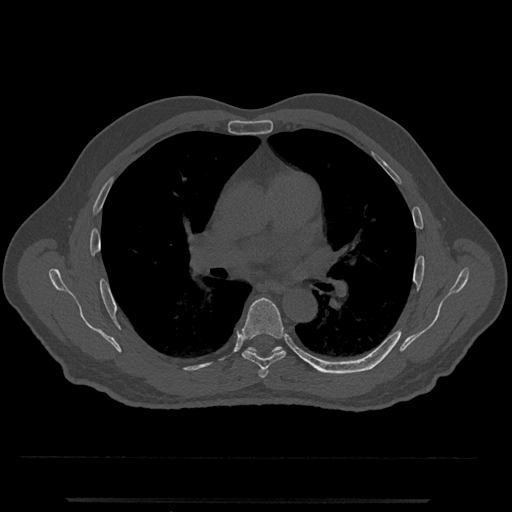
CT including the spine, one axial slice; position 729 of 797 along the scan axis; bone window (W 1800 / L 400 HU); 0.5 mm slice thickness; 512 × 512 image matrix, field of view 419 × 419 mm. Patient: male, 63 years. From the clinical record (not read from this slice): primary cancer: prostate.
Annotated regions visible in this slice (semi-automatically segmented with operator editing):
- T5 vertebra: box from (x=259, y=369) to (x=269, y=378) px
- T6 vertebra: (x=241, y=298)–(x=286, y=370)
- T7 vertebra: (x=247, y=346)–(x=324, y=373)